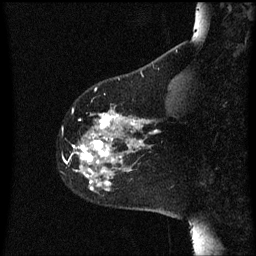
Breast MRI (dynamic contrast-enhanced), one sagittal slice. Position 15 of 60 along the scan axis. Dynamic contrast-enhanced series, image 2 of 3 at this slice position (ordered by acquisition). 1.5 T. TE 4.2 ms, TR 8 ms. 2 mm slice thickness. 256 × 256 image matrix, field of view 200 × 200 mm. Female patient, age 60 years.
Annotated regions visible in this slice (semi-automatic segmentation, software-assisted and operator-edited):
- analysis volume of interest (the breast-tissue region the enhancement analysis was run in; not a lesion): bounding box (x1, y1, x2, y2) in pixels: (65, 108, 158, 193)
- tumour enhancement mask (voxels above the 70 % enhancement threshold inside the analysis volume of interest): (73, 110, 158, 191)